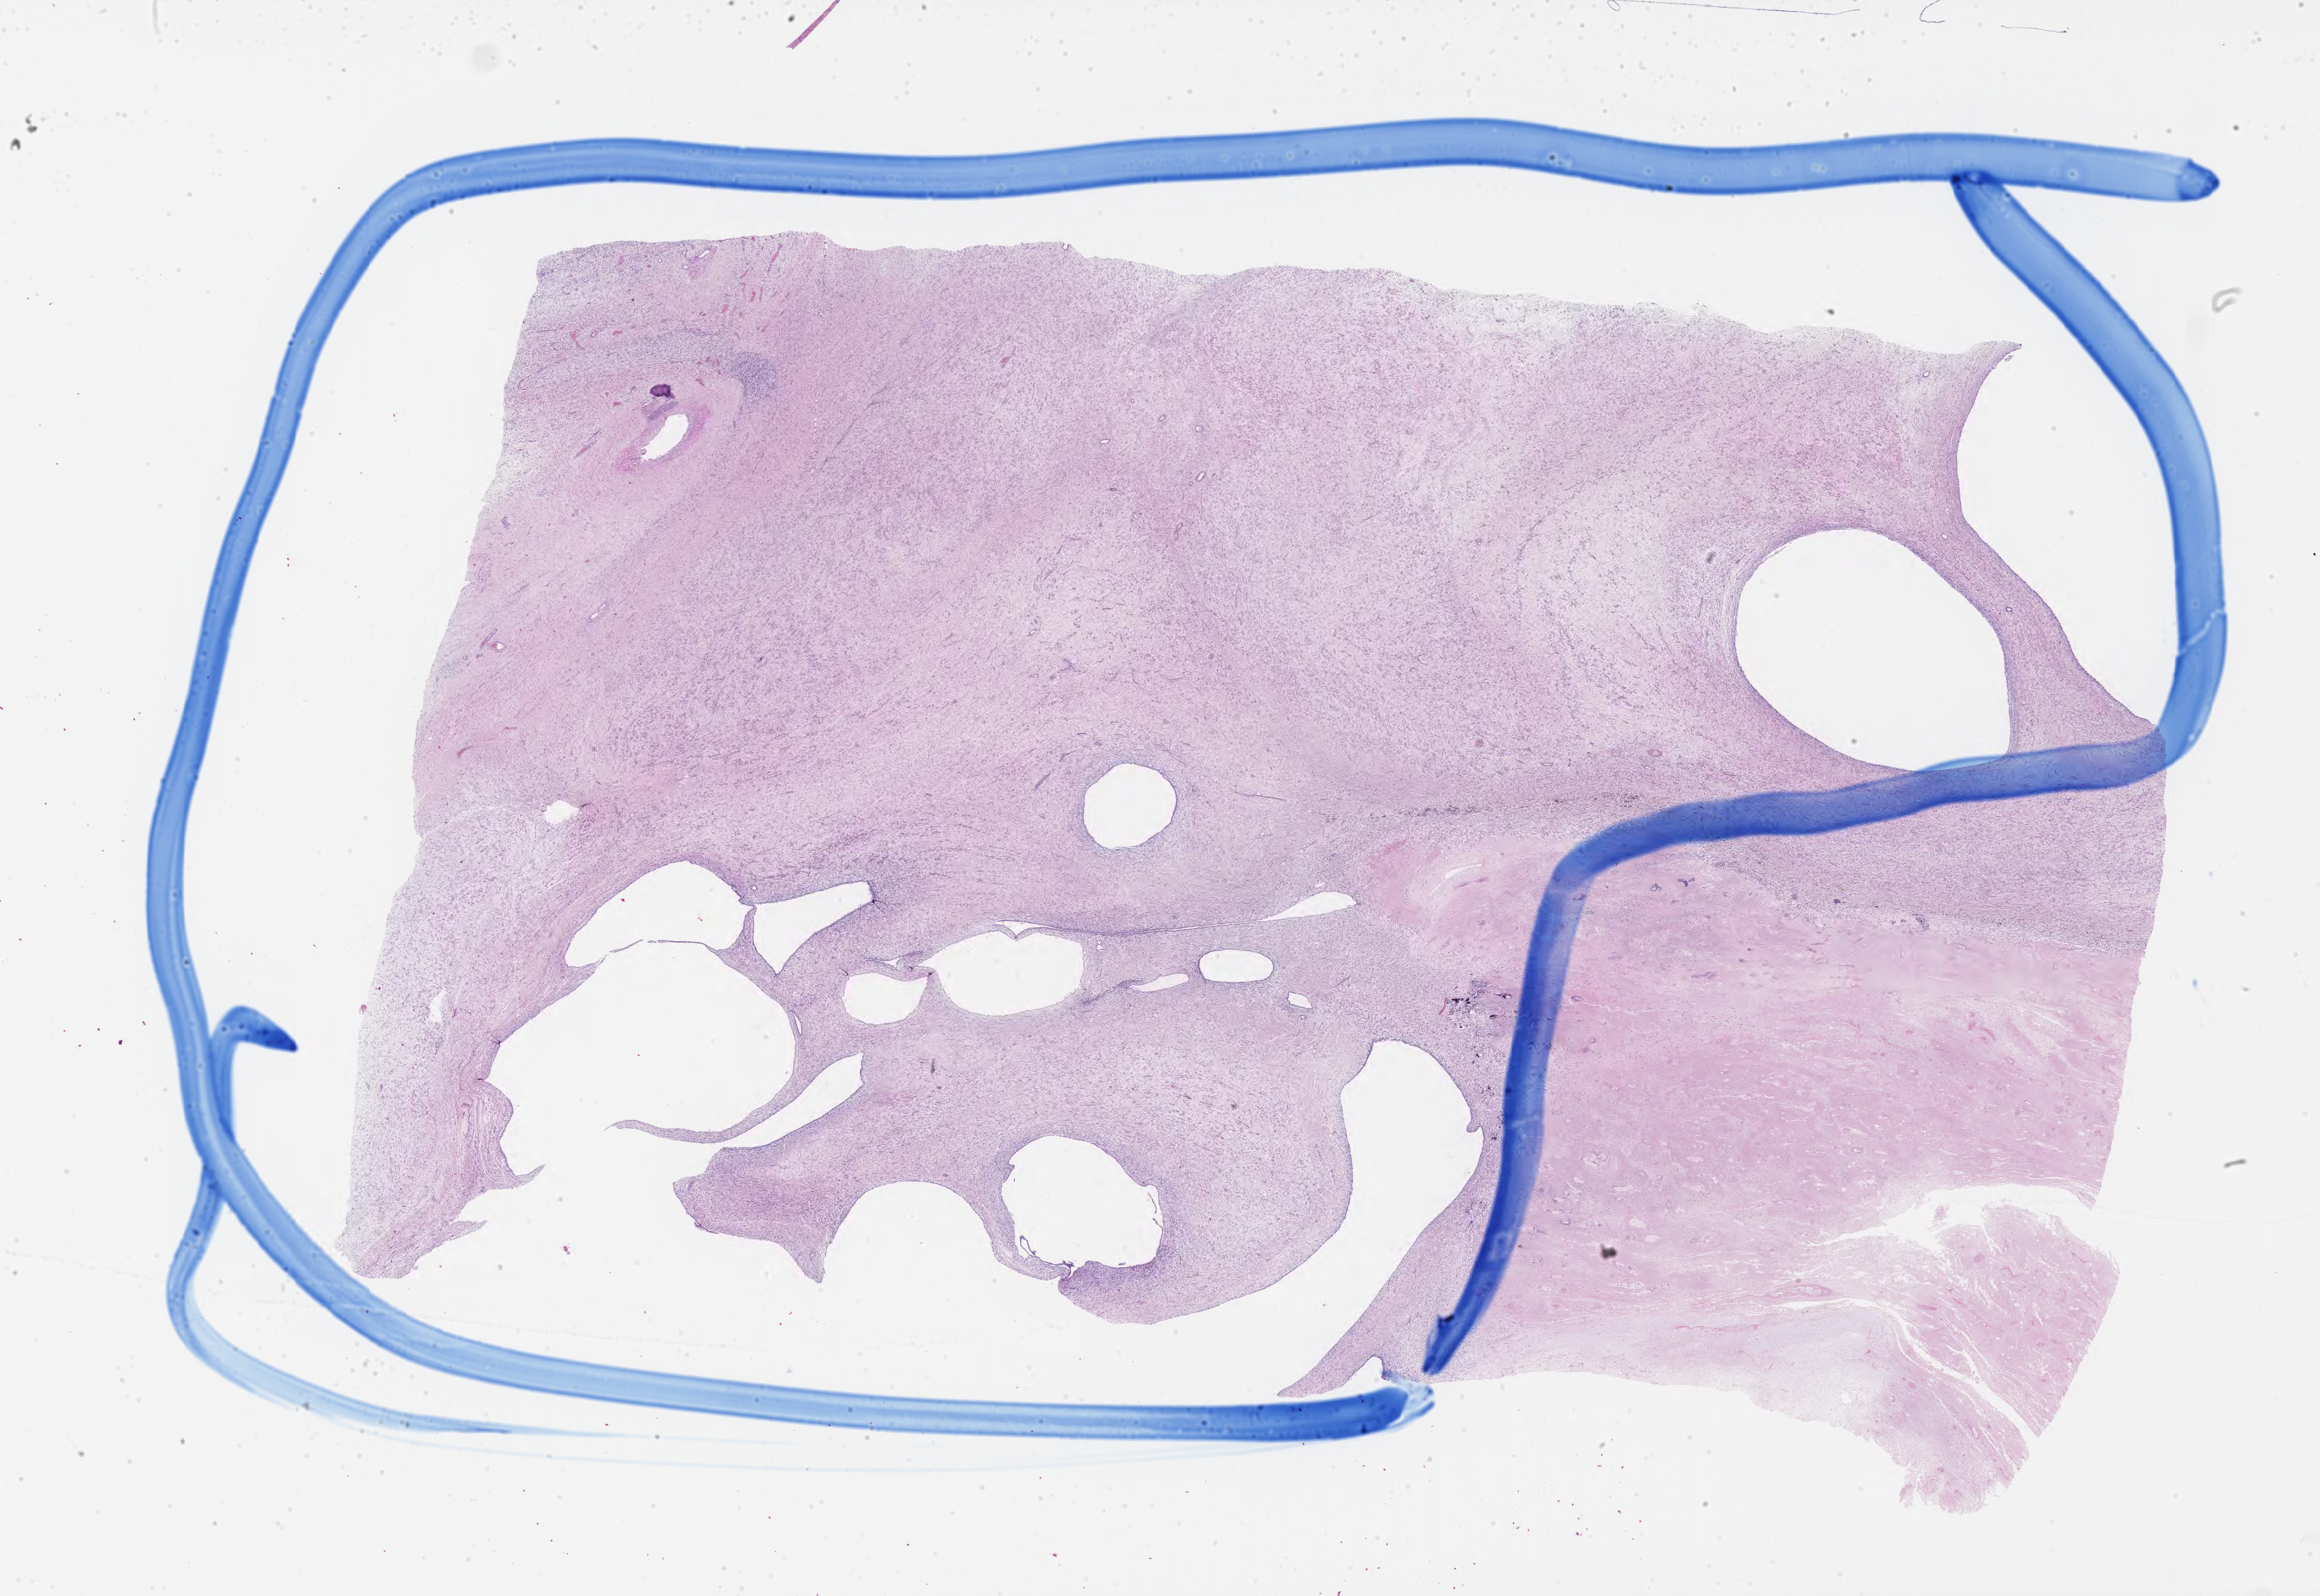
Whole-slide image, hematoxylin and eosin (H&E) stain, a low-resolution overview of the entire scanned area, about 31.7 x 21.8 mm, formalin-fixed paraffin-embedded section, specimen: primary tumor, anatomic site: kidney (left). Male patient; age at initial diagnosis 1 years. Composition of this section per pathologist review: tumor cells 80%, tumor nuclei 90%, stromal cells 0%, necrosis 20%, normal cells 0%. Infiltration values recorded for this section: lymphocyte infiltration 0%, monocyte infiltration 0%, neutrophil infiltration 0%.
Histologic diagnosis: Nephroblastoma, NOS. Section: bottom of the tissue portion.